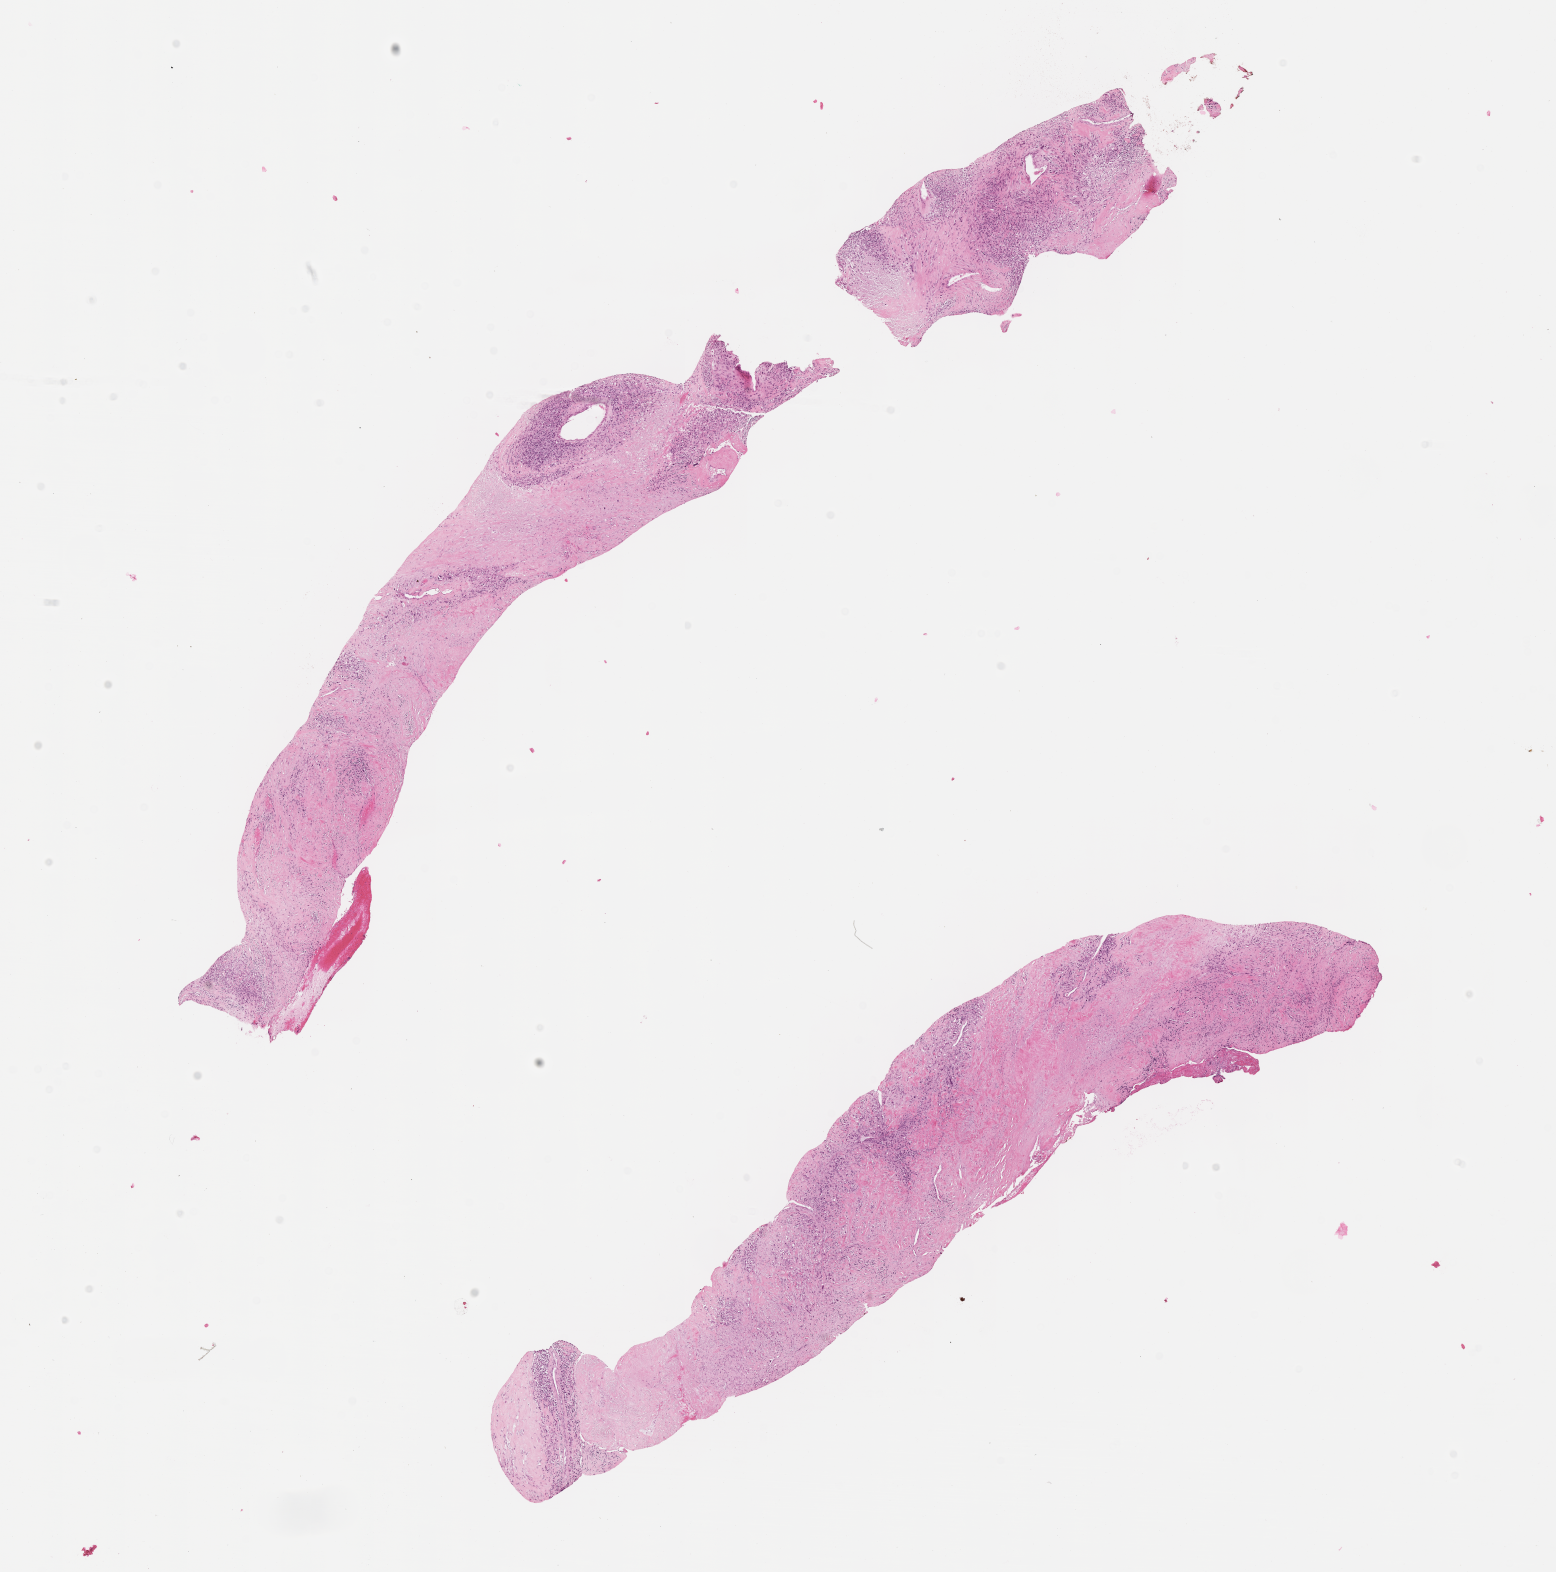
Haematoxylin and eosin whole-slide image of tumor tissue, whole scanned area (about 12.6 x 12.7 mm) shown as a low-resolution overview, FFPE section, site: retroperitoneum. Female patient, age at diagnosis 2.9 years.
Metastatic status at presentation (as recorded): non-metastatic (confirmed). Diagnosis: rhabdomyosarcoma; histological classification: embryonal rhabdomyosarcoma. Stage (as recorded): 3.